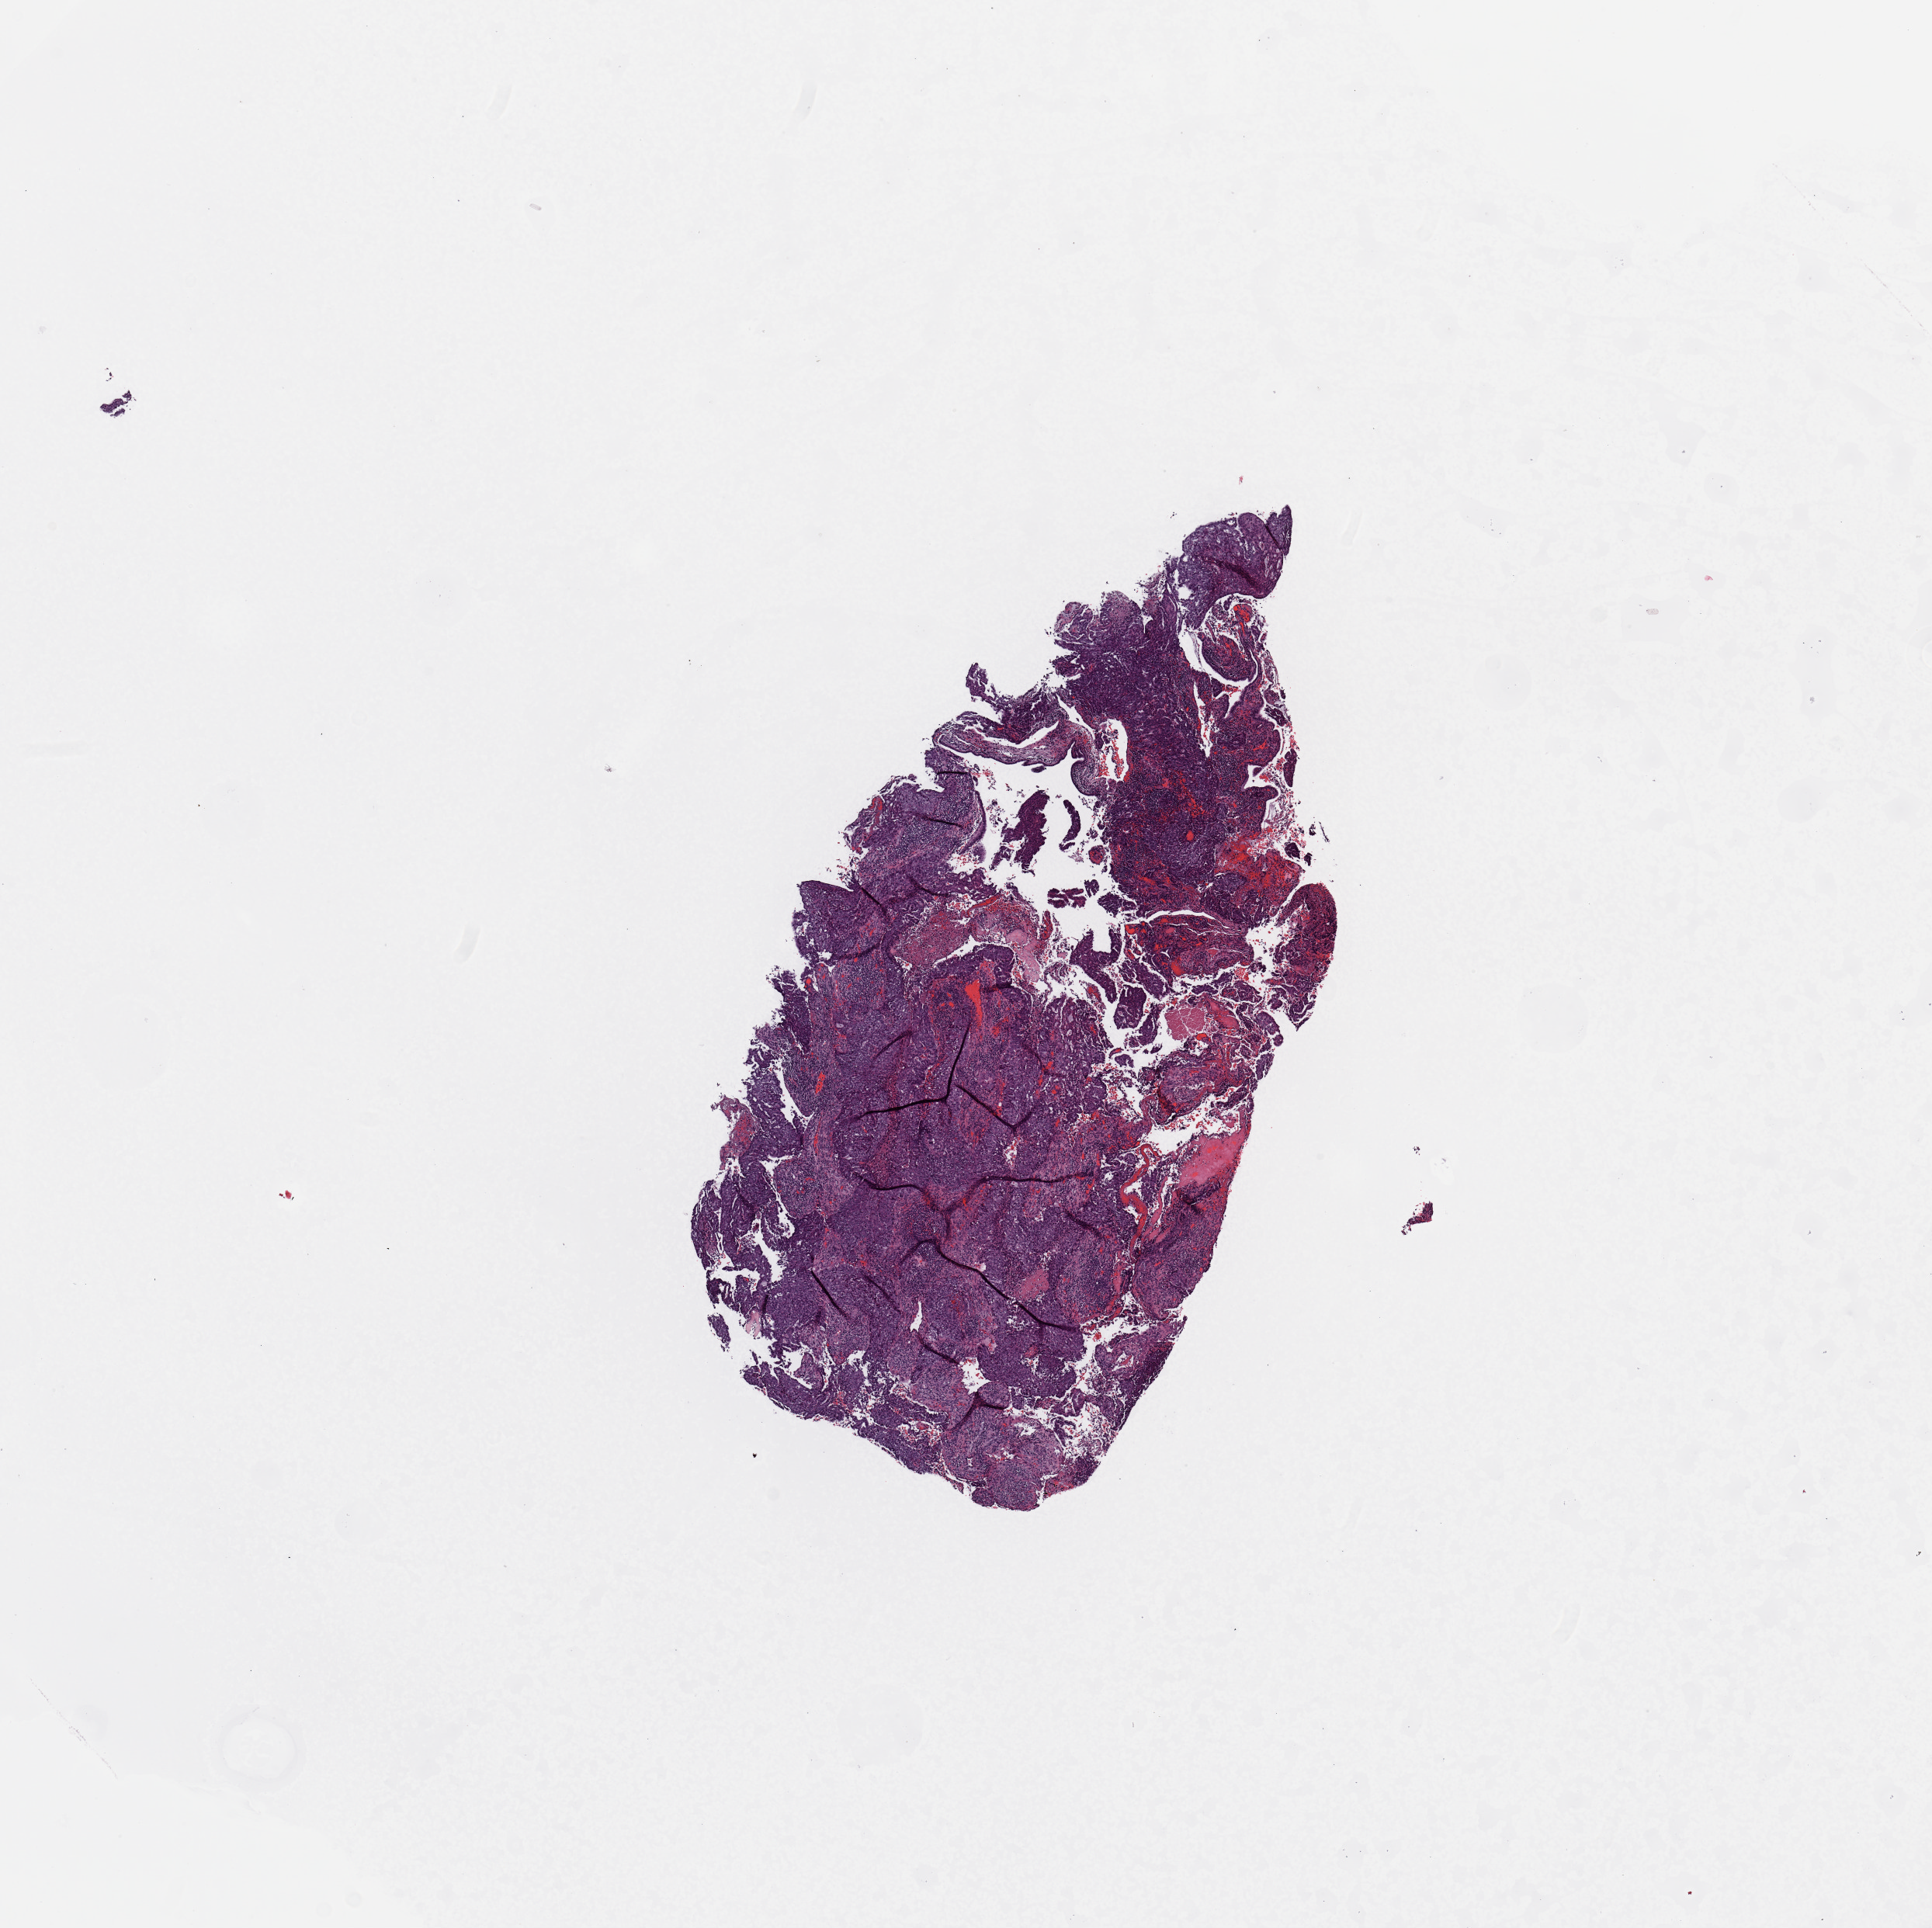
Hematoxylin and eosin (H&E) stained whole-slide image — whole scanned area (about 9.8 x 9.8 mm, from a 20x scan) shown as a low-resolution overview. Uterus, tumour tissue. Female, 48 y/o. Histologic grade: G3 (poorly differentiated).
* diagnosis: Endometrioid adenocarcinoma, NOS
* AJCC pathologic stage: II